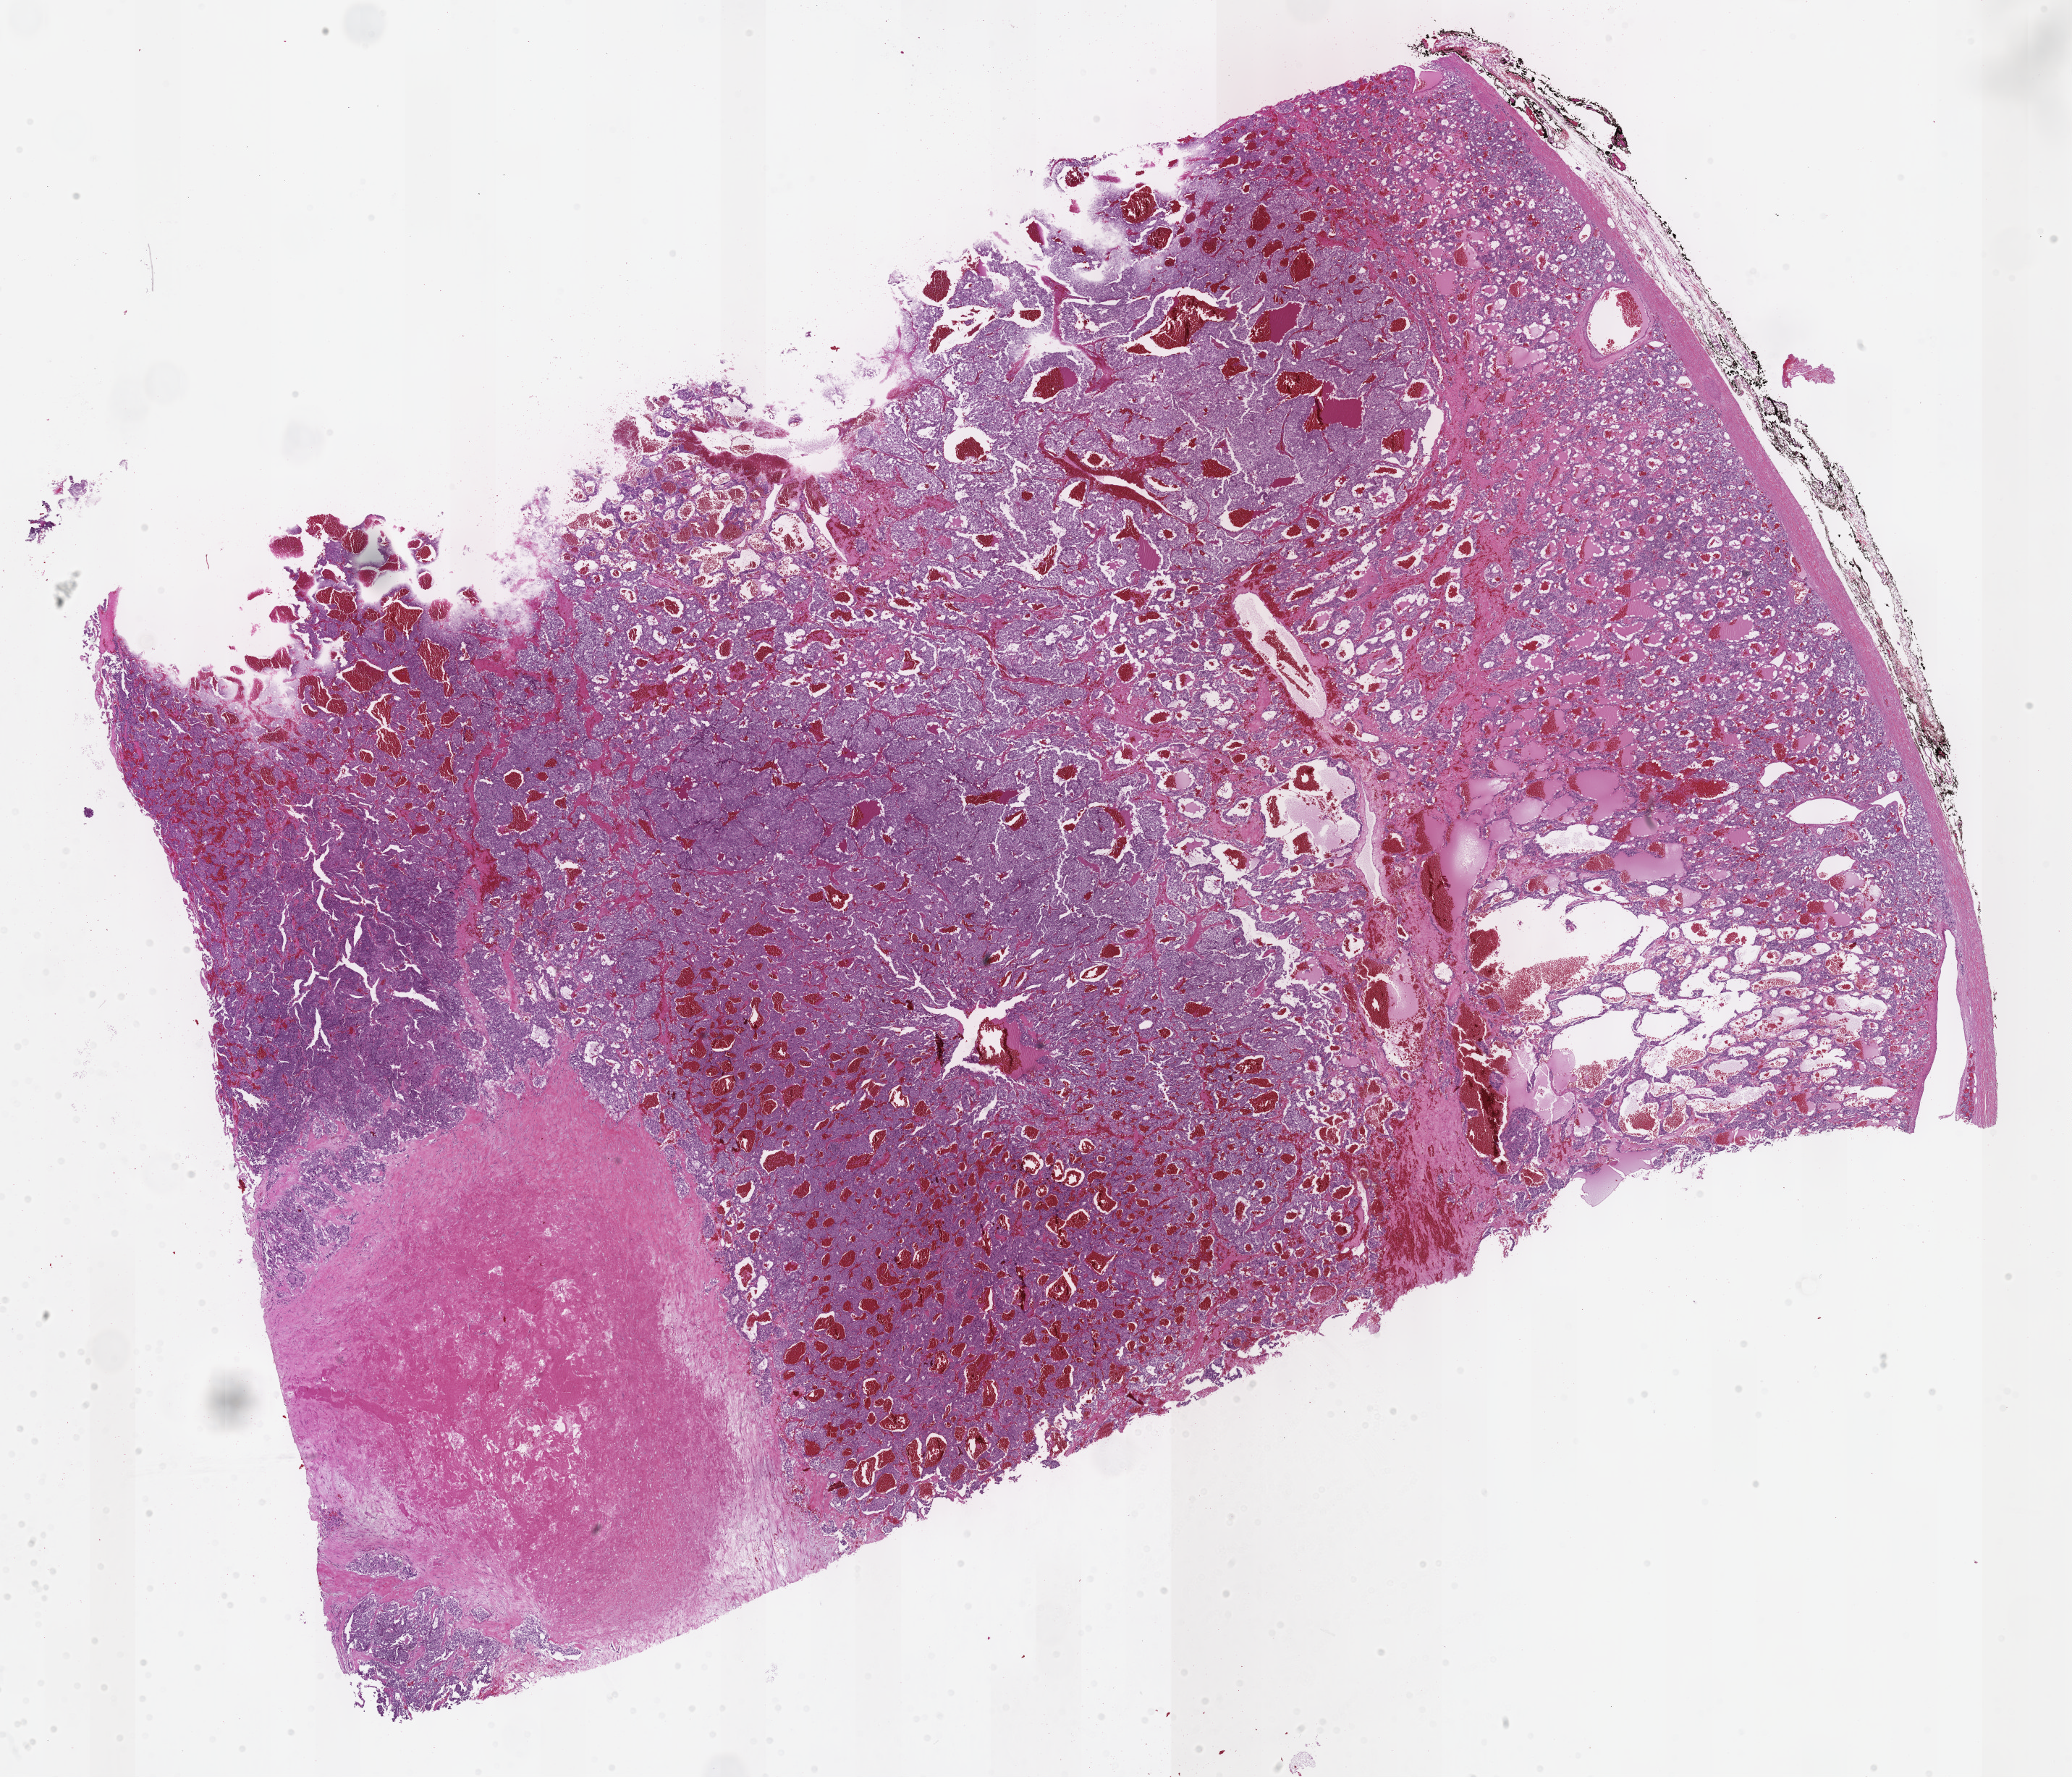
Digitized H&E tissue section (whole slide) — low-resolution overview of the scanned area, about 23.2 x 19.9 mm (slide scanned at 40x); FFPE section; sample: primary tumour, adrenal gland. Patient: female, age at initial diagnosis 51 years.
Histologic diagnosis: Pheochromocytoma, NOS.